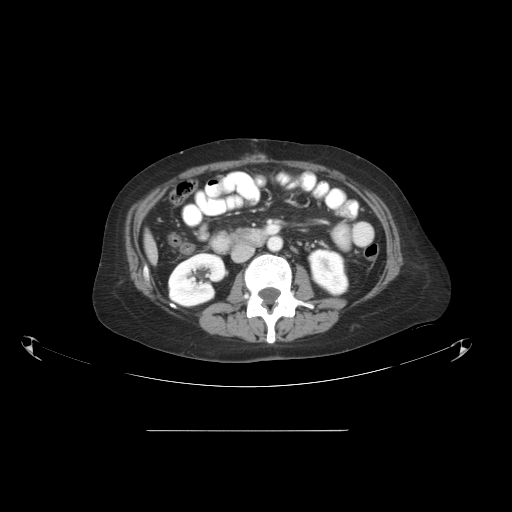
Contrast-enhanced abdominal CT, one axial slice; slice 19 of 51 in the series (ordered by position); reconstruction kernel STANDARD; intravenous contrast given; soft-tissue window (W 400 / L 40 HU); 5 mm slice thickness; 512 × 512 image matrix. Female patient, age 48 years. From the clinical record (not read from this slice): diagnosis: colorectal cancer liver metastases, imaged before liver resection; multiple liver metastases: yes; largest metastasis: 1 cm; chemotherapy before resection: no.
Structures marked on this image (manually delineated by an expert):
- liver: bounding box <145,235,157,261> (left, top, right, bottom; pixels)
- planned liver remnant (the part of the liver to remain after resection): <145,234,158,262>